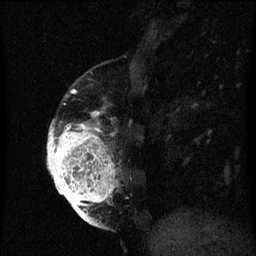
Breast MRI (dynamic contrast-enhanced), one sagittal slice; position 18 of 60 along the scan axis; dynamic contrast-enhanced series, image 2 of 3 at this slice position (ordered by acquisition); 1.5 T; TE 4.2 ms, TR 8 ms; 2 mm slice thickness; 256 × 256 image matrix, field of view 180 × 180 mm. Patient: female, 56 years.
Outlined on this slice (semi-automatic segmentation, software-assisted and operator-edited):
- analysis volume of interest (the breast-tissue region the enhancement analysis was run in; not a lesion): bounding box [x1, y1, x2, y2] px = [48, 96, 121, 219]
- tumour enhancement mask (voxels above the 70 % enhancement threshold inside the analysis volume of interest): [48, 112, 117, 219]